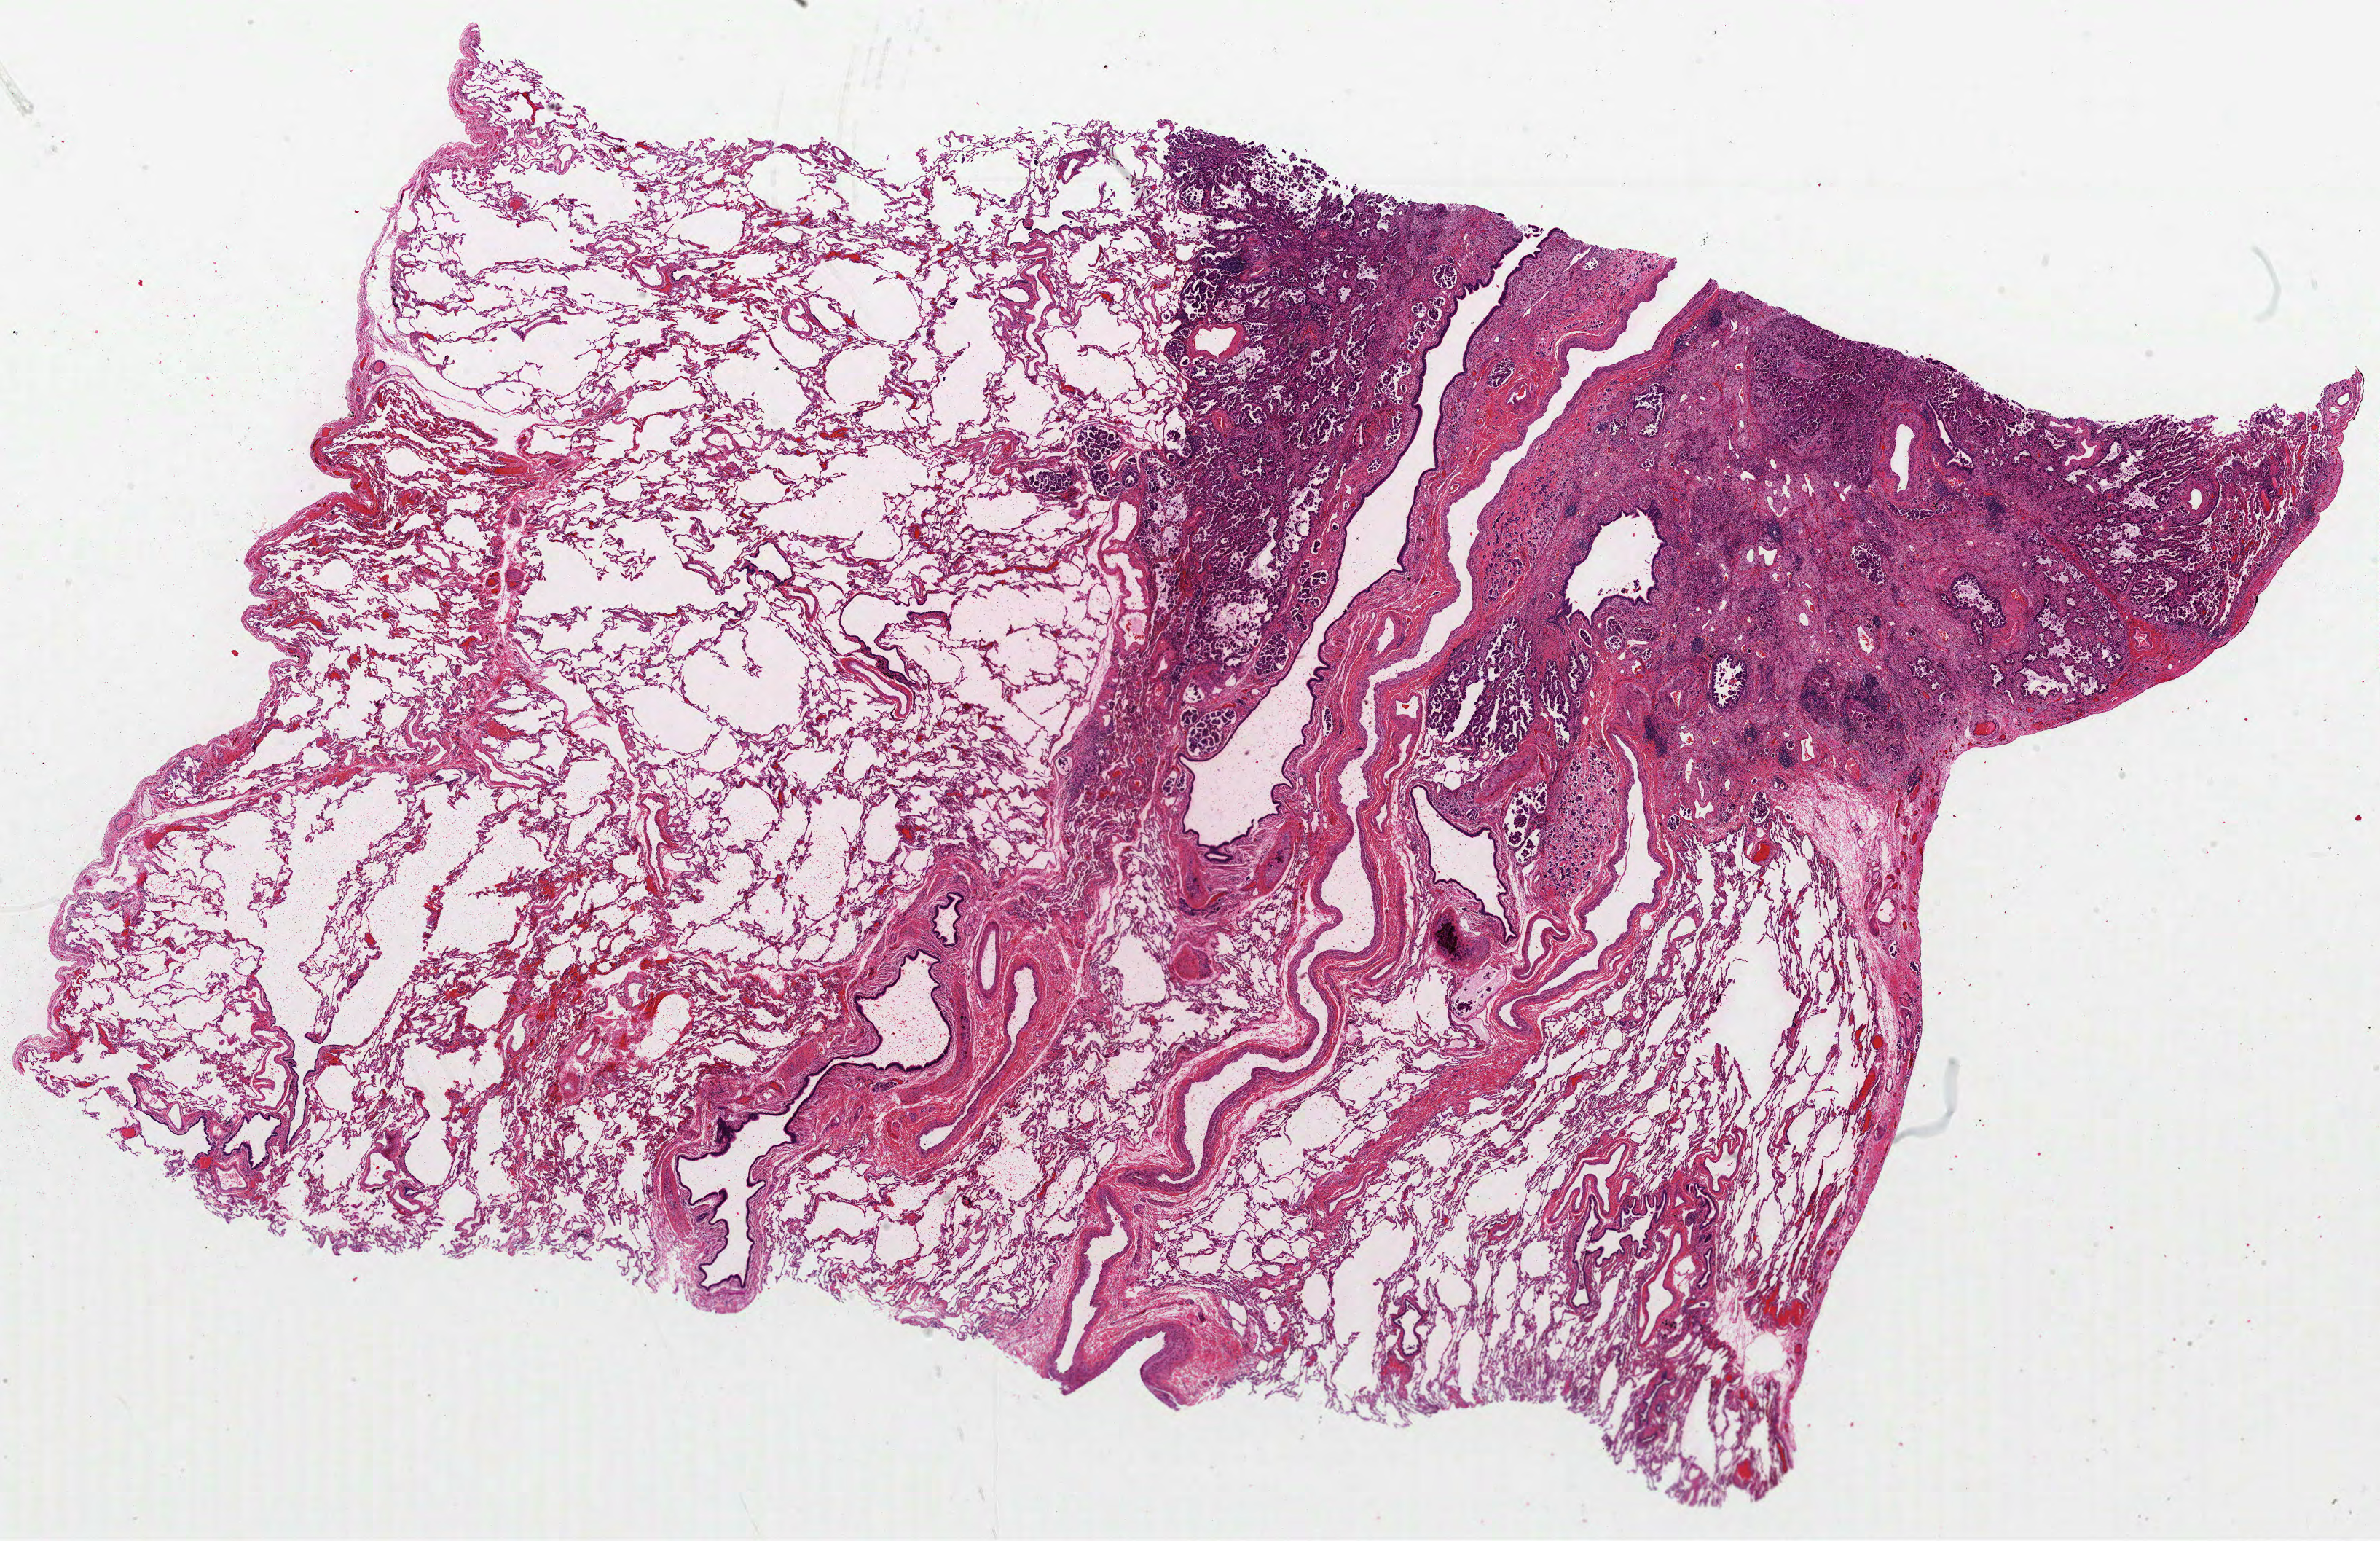
H&E-stained whole-slide image — shown as a low-resolution overview of the whole scanned area (about 26.3 x 17.1 mm, slide scanned at 40x); FFPE section; sample: primary tumour, lung. Female, age 69 years at initial diagnosis.
Laterality: right. AJCC pathologic stage: IIIA. TNM: T2 N2 MX. Pathologic diagnosis: Adenocarcinoma, NOS (middle lobe, lung).